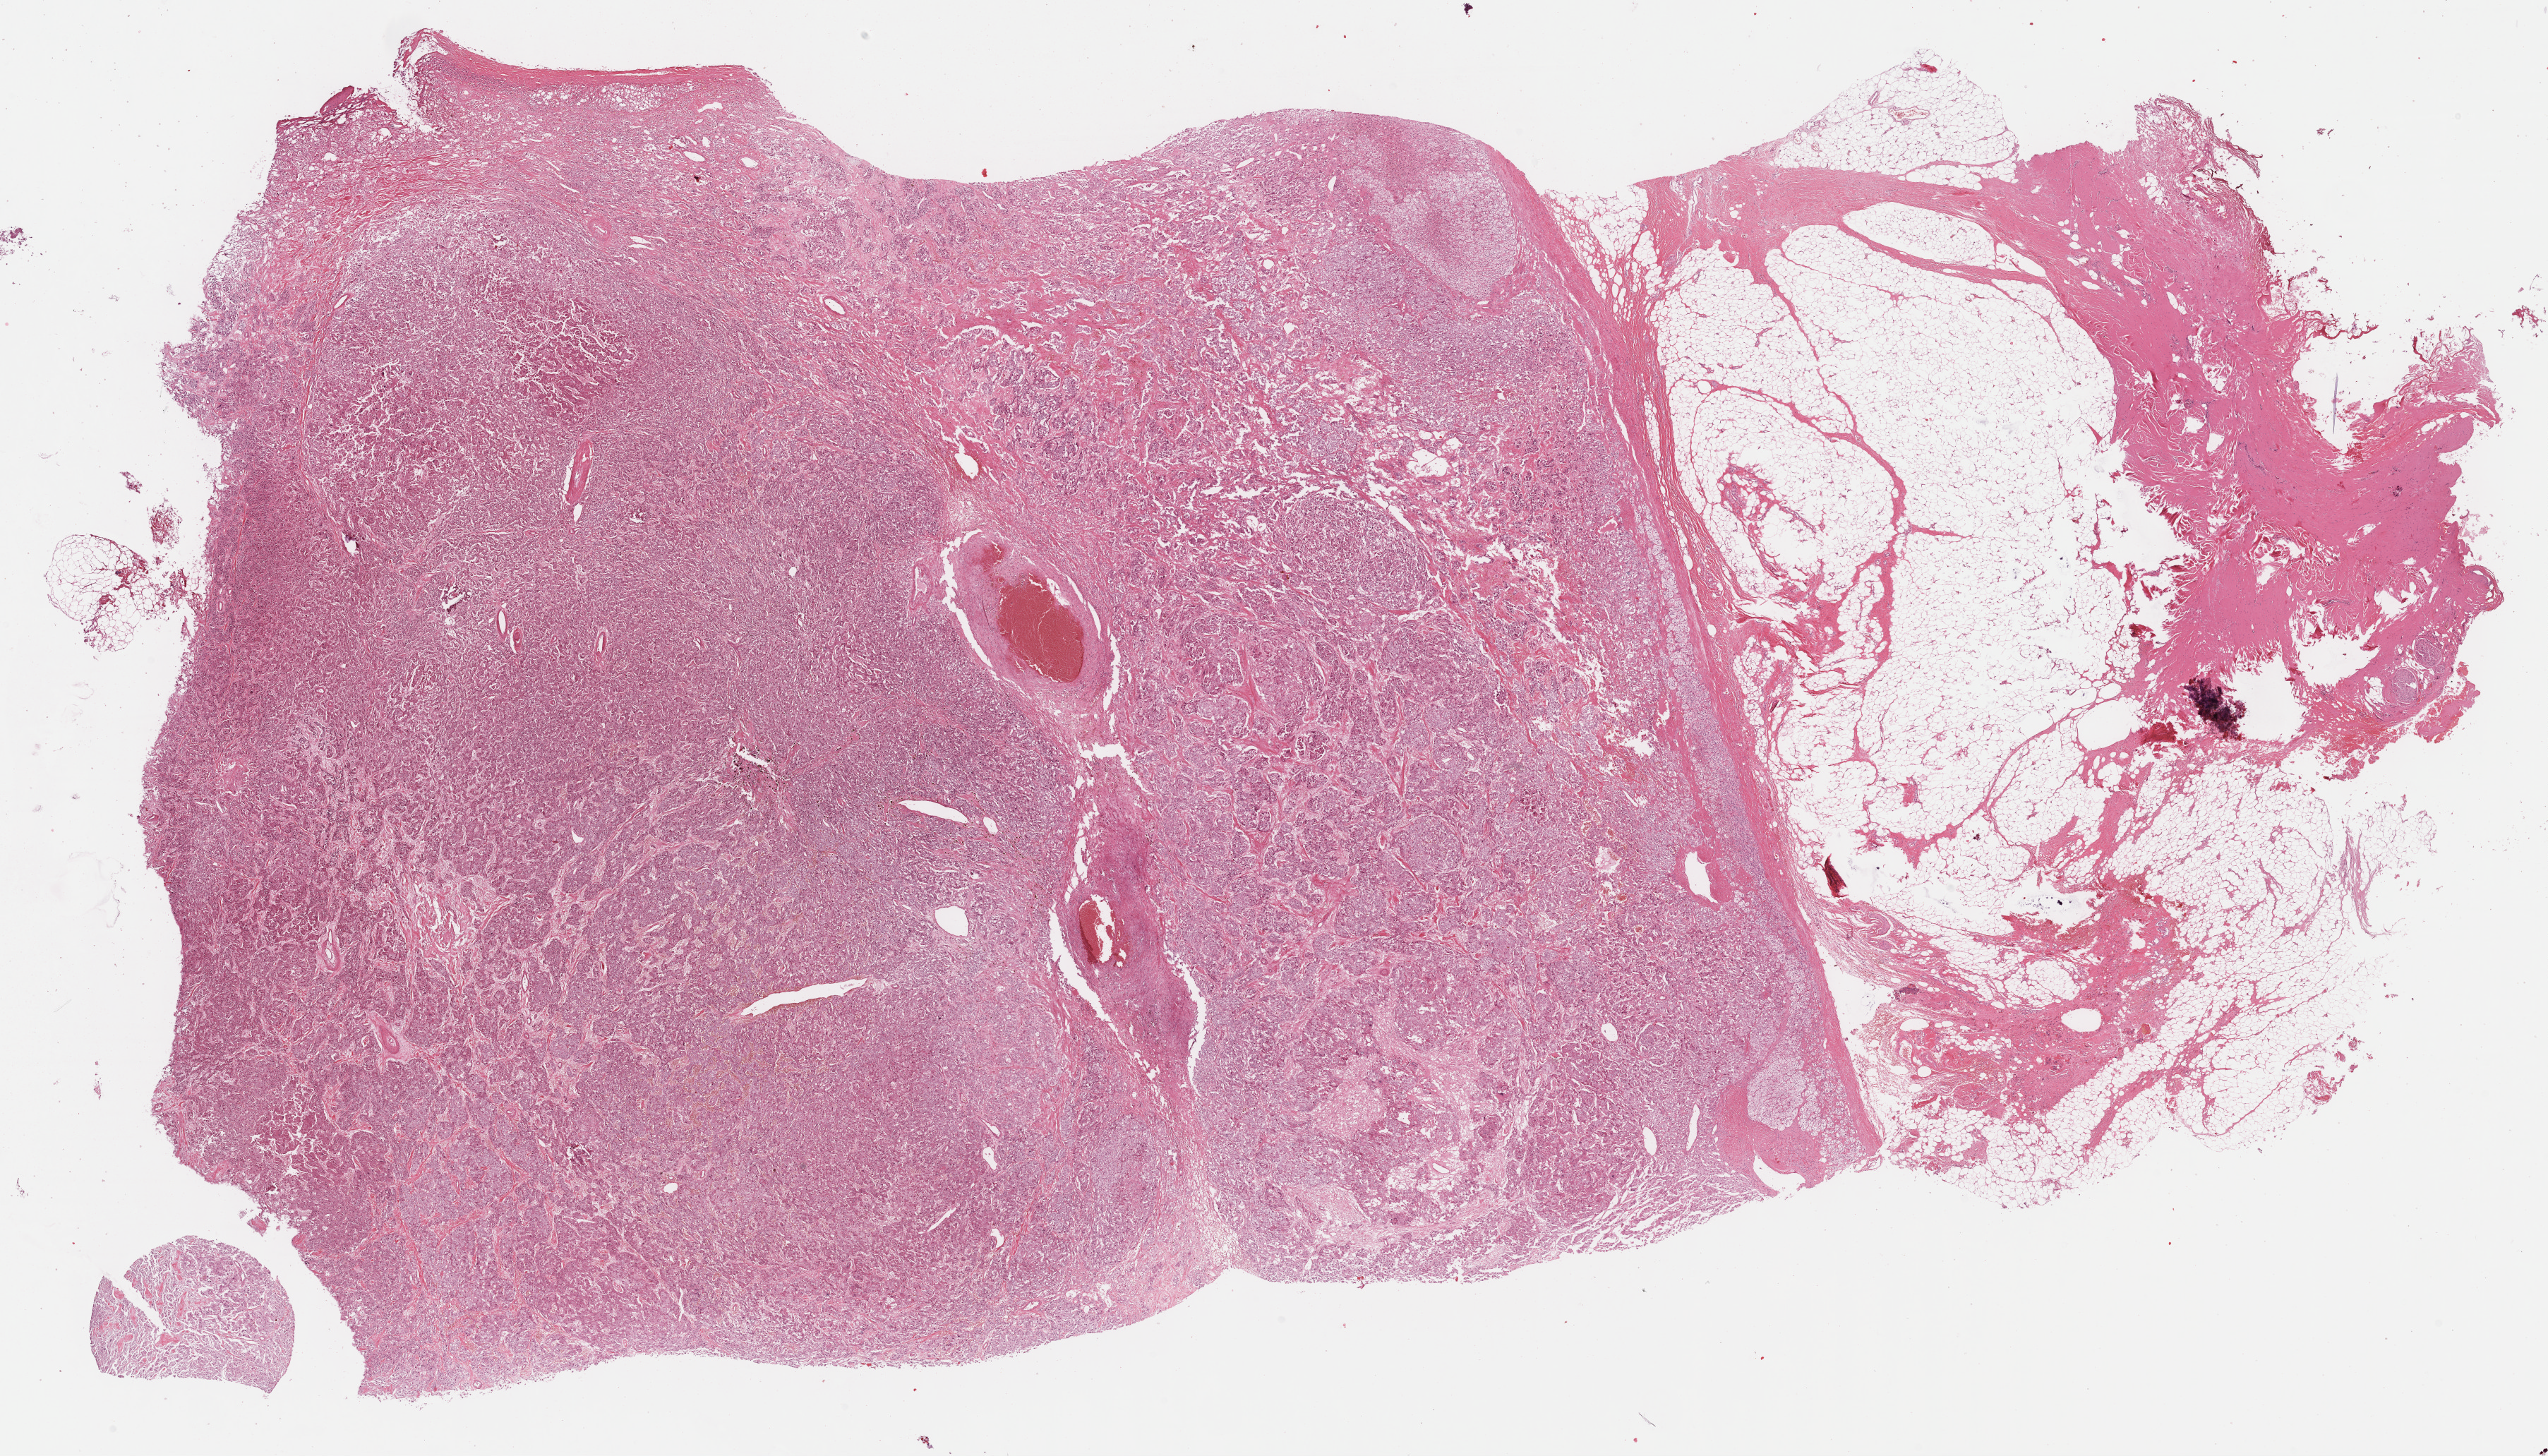
Digitized H&E tissue section (whole slide) — shown as a low-resolution overview of the whole scanned area (about 29.2 x 16.7 mm), FFPE section, adrenal gland, primary tumour sample. Patient: male, age at initial diagnosis 76 years.
Diagnosis: Pheochromocytoma, malignant.